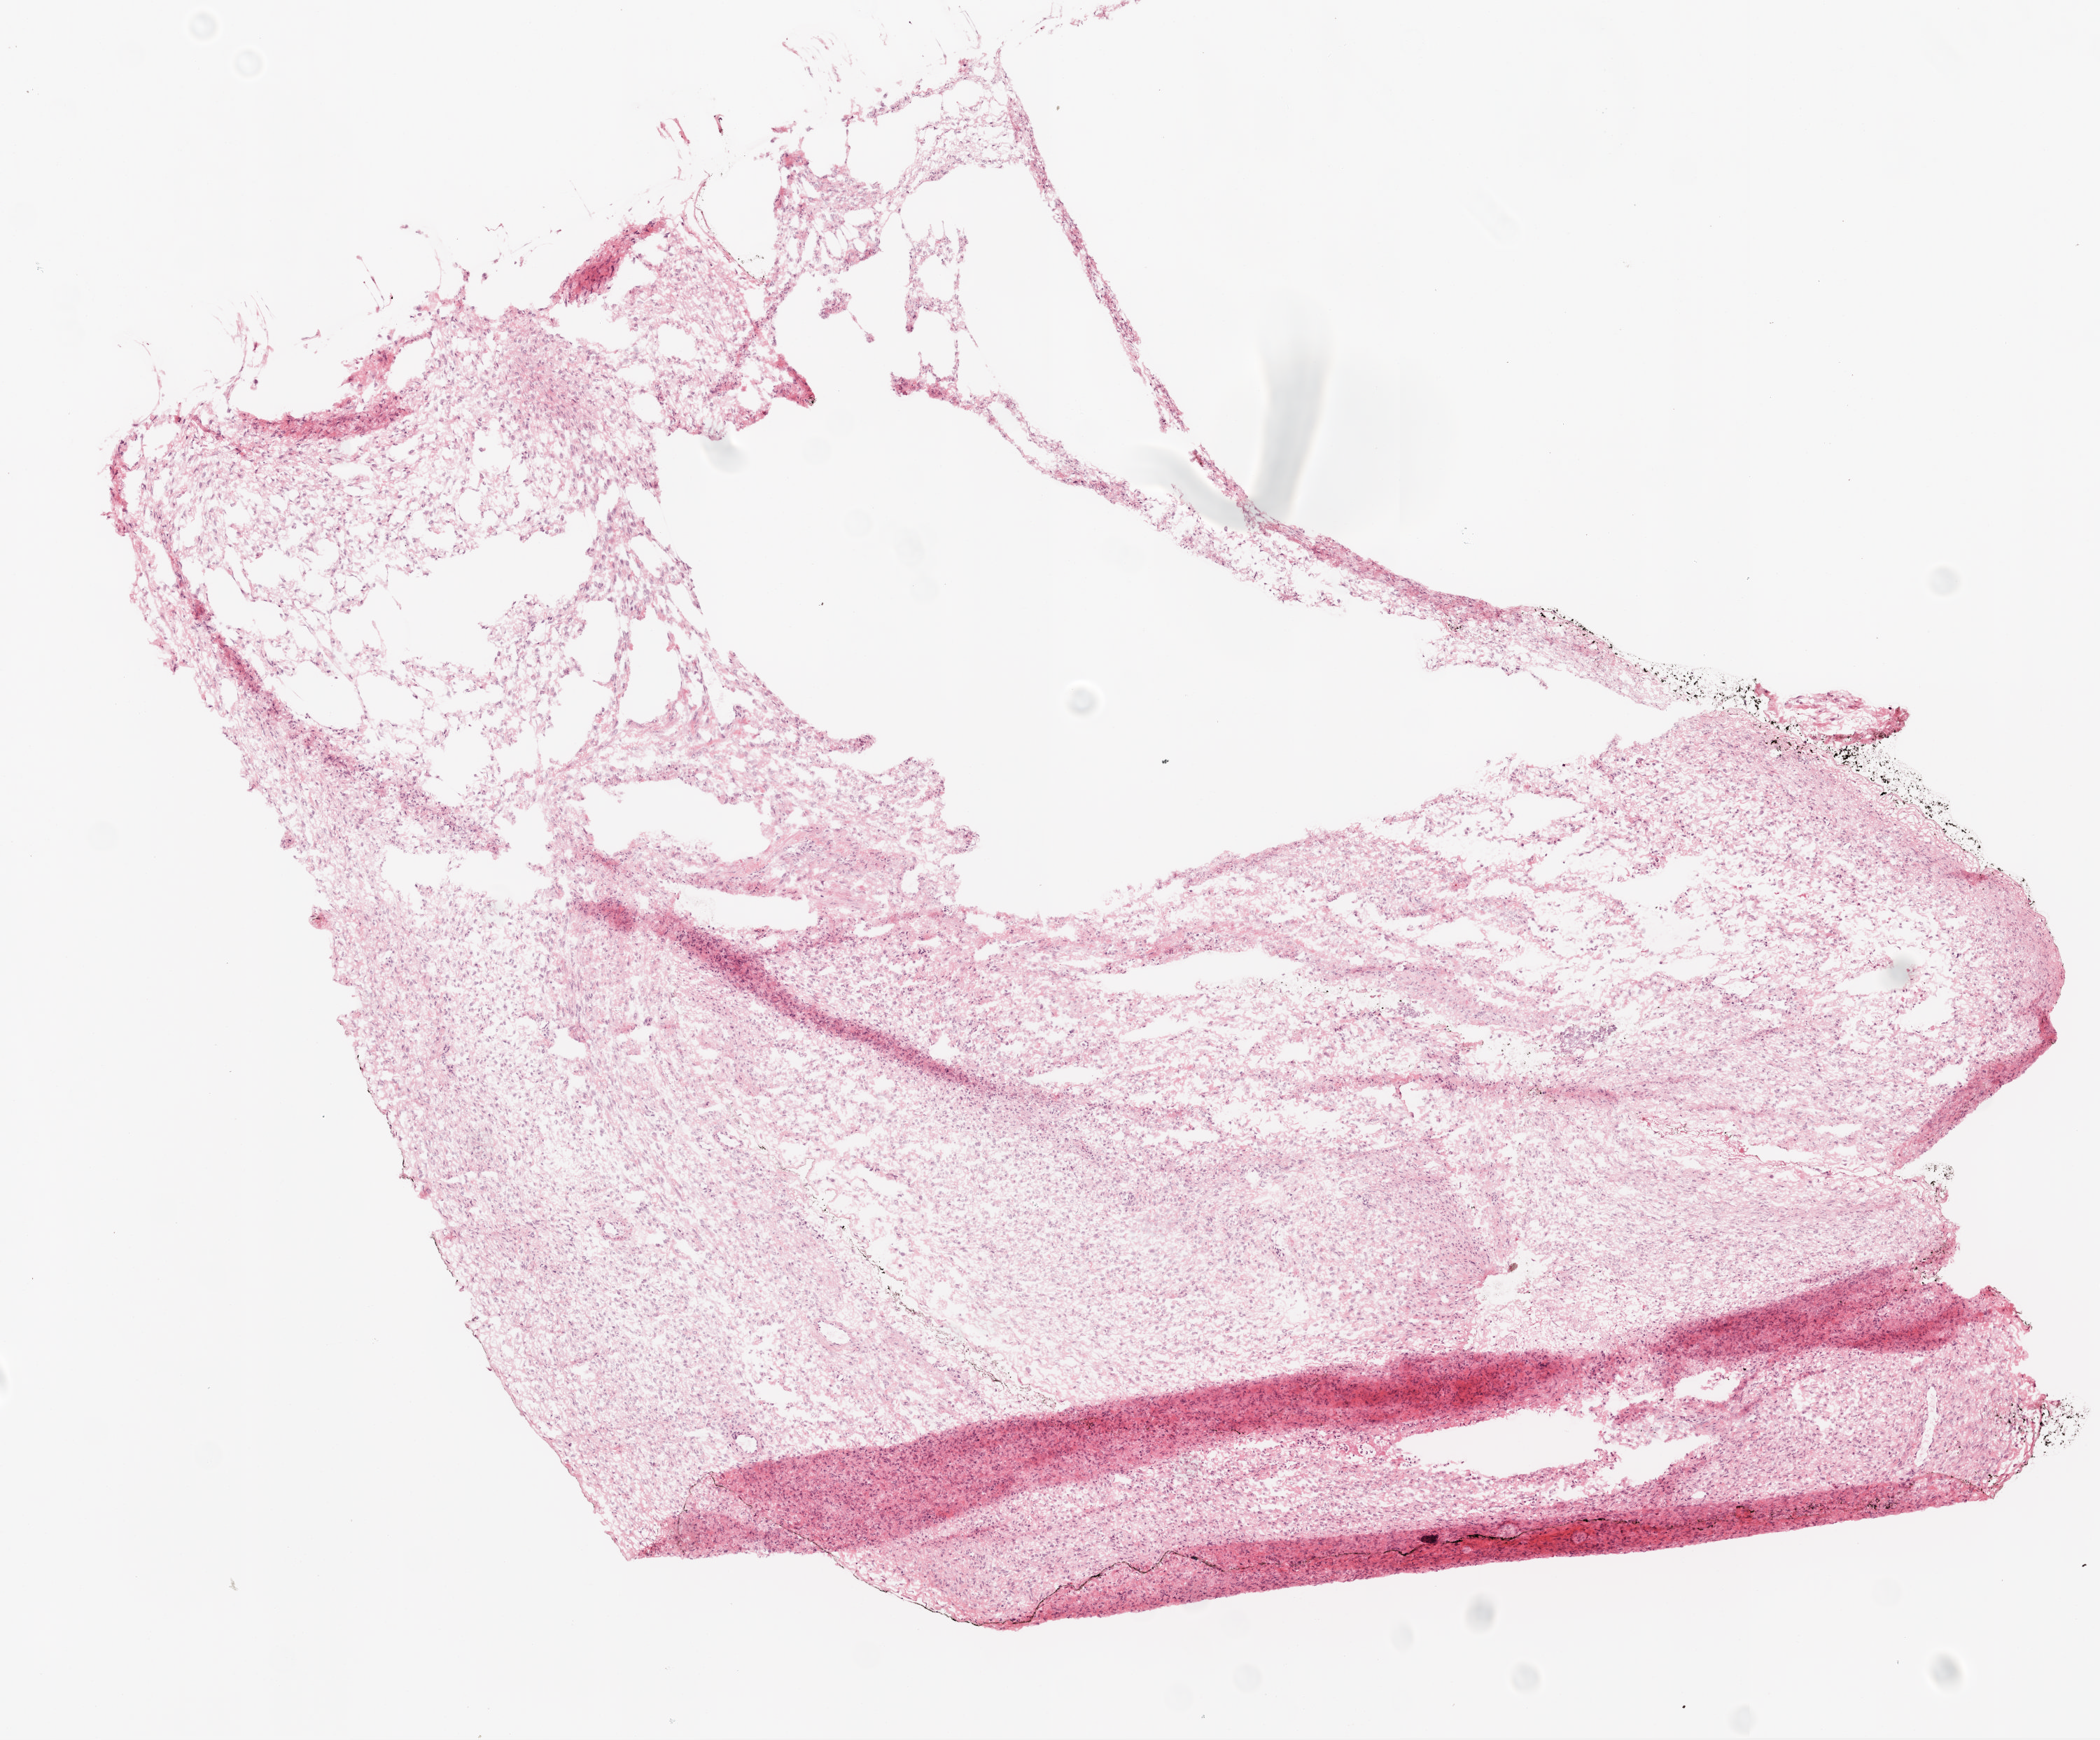
Hematoxylin and eosin (H&E) stained whole-slide image, whole scanned area (about 6.0 x 5.0 mm, acquisition: 20x scan) shown as a low-resolution overview, frozen section from the top of the tissue portion, ovary, solid tissue normal (non-tumour tissue) sample. Female, age 63 years at initial diagnosis.
• this section: solid tissue normal sample (biorepository sample class)
• patient diagnosis: Serous cystadenocarcinoma, NOS